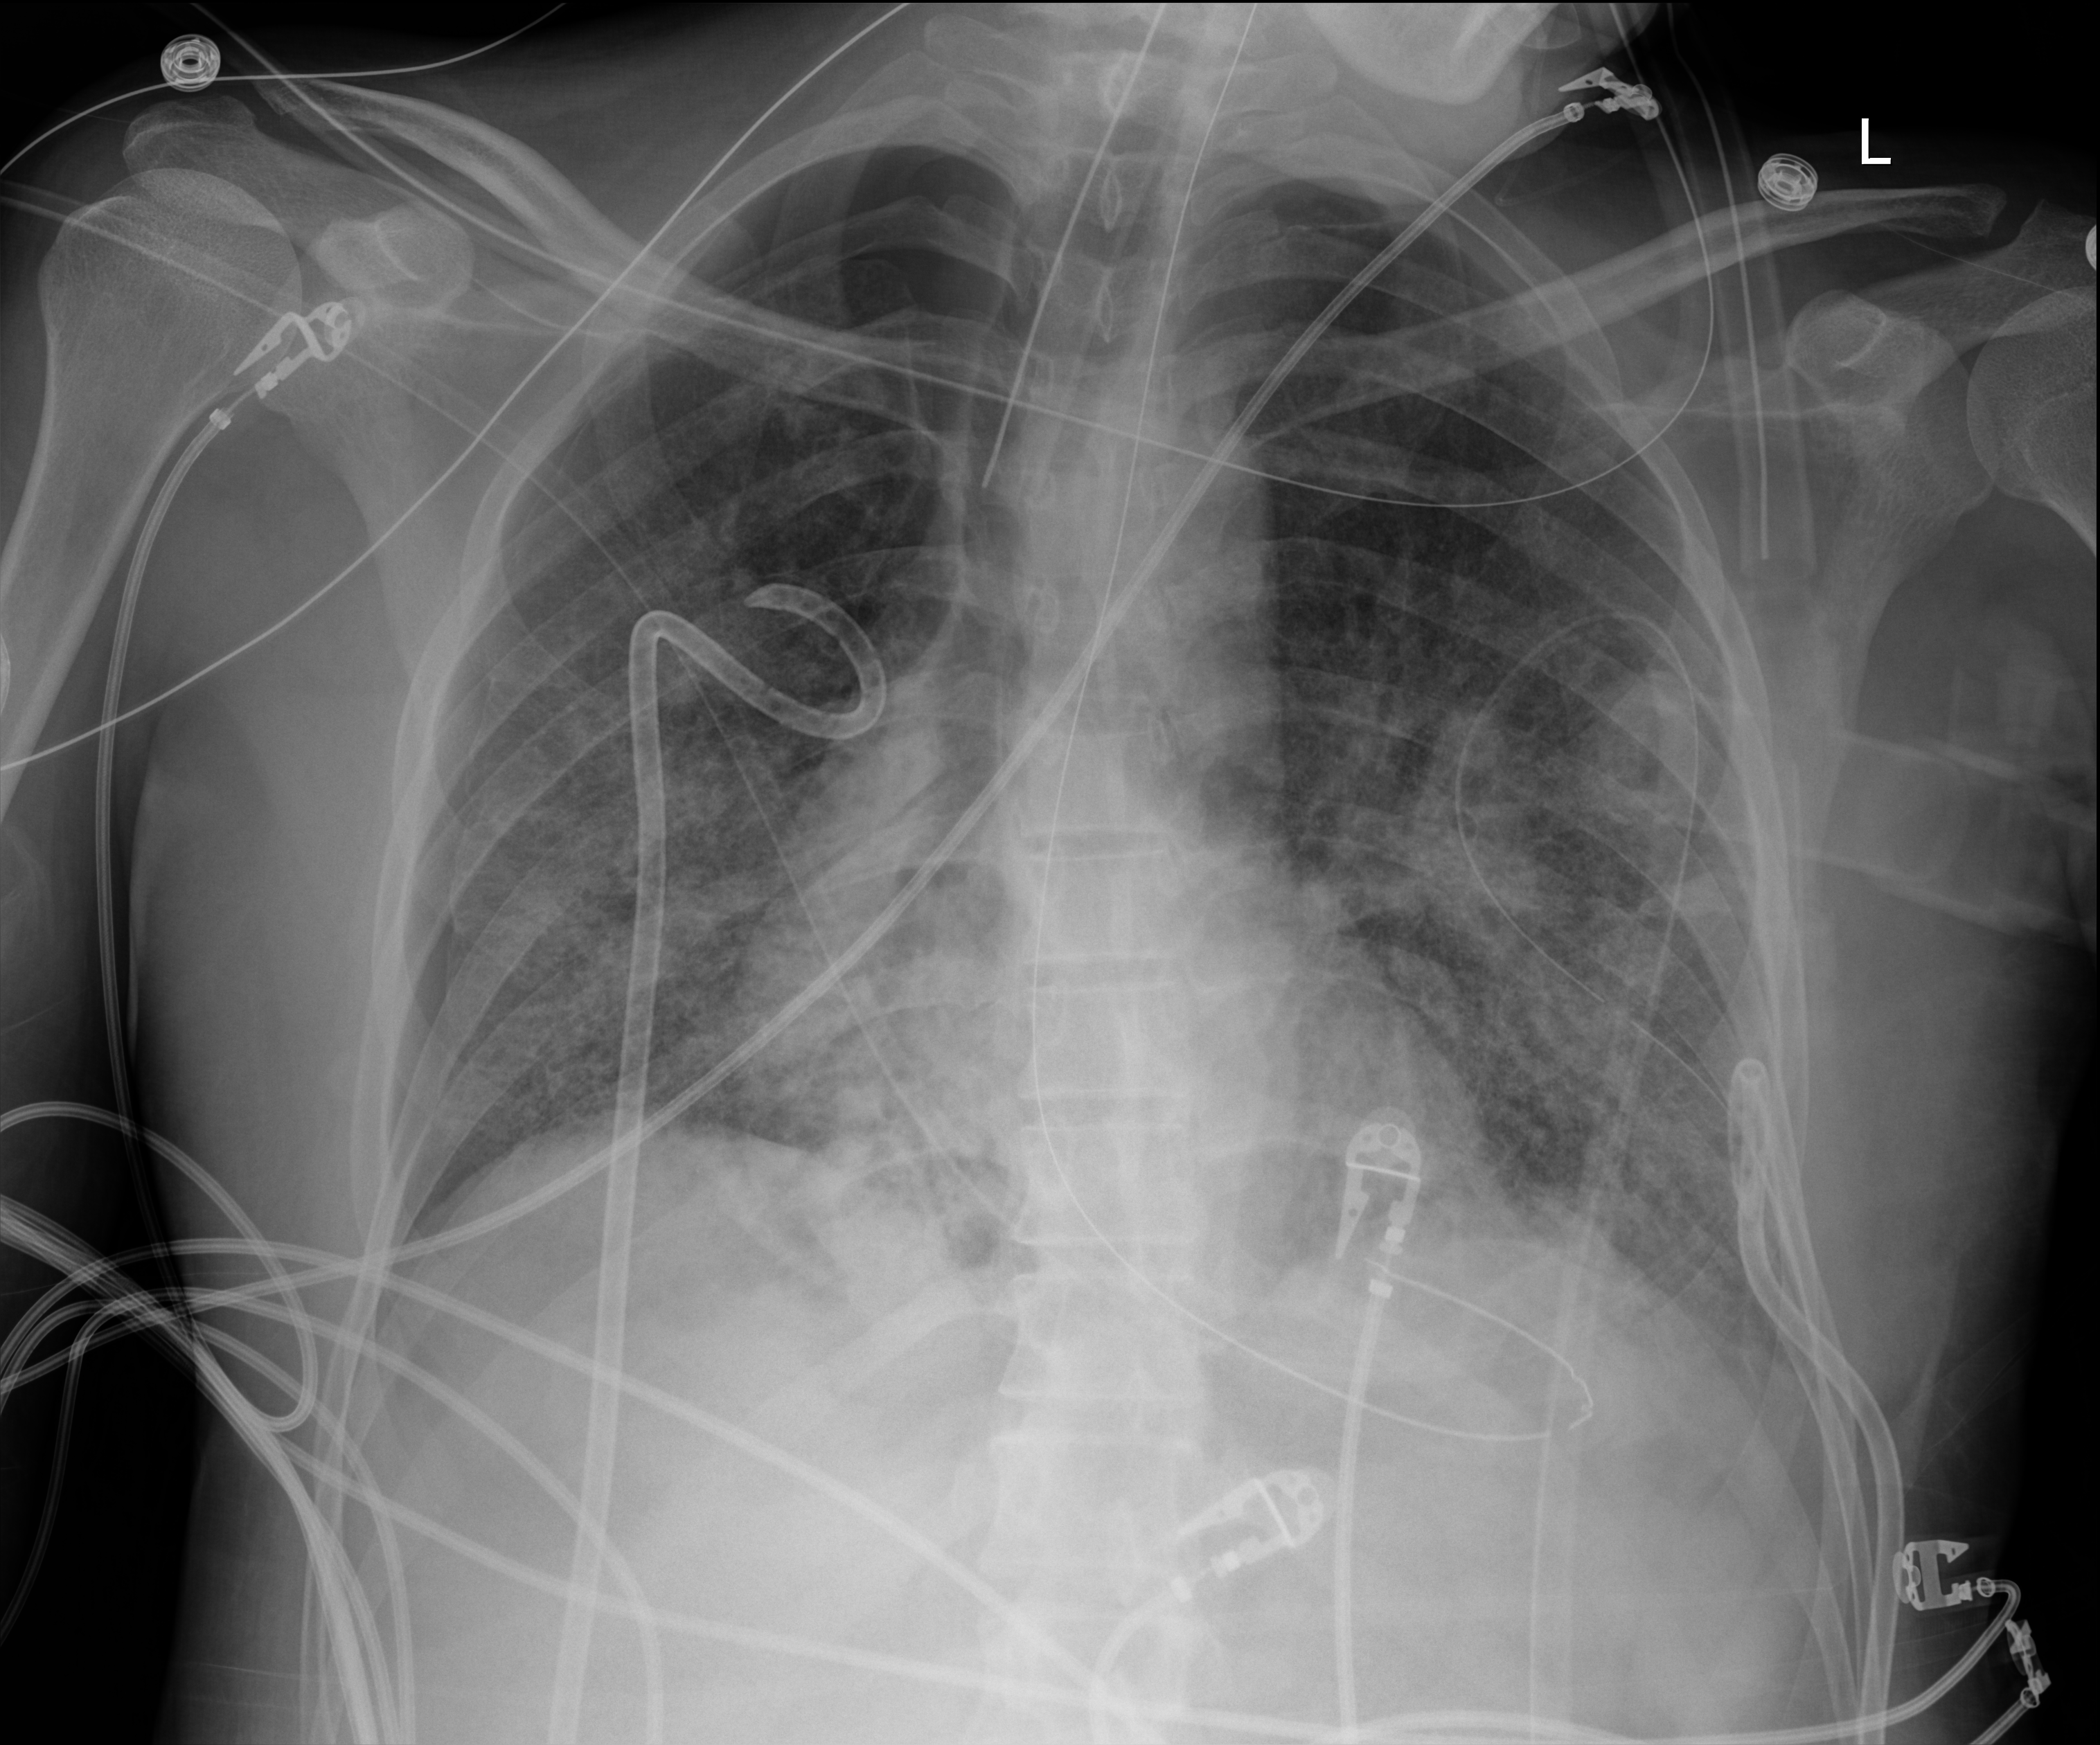
Chest radiograph (digital radiography), anteroposterior (AP) projection. Adult patient hospitalised with COVID-19, age 18–59 years.
Admission-level facts for this patient (not findings on this image; timing relative to this image not recorded): chronic kidney disease (admission record): no.